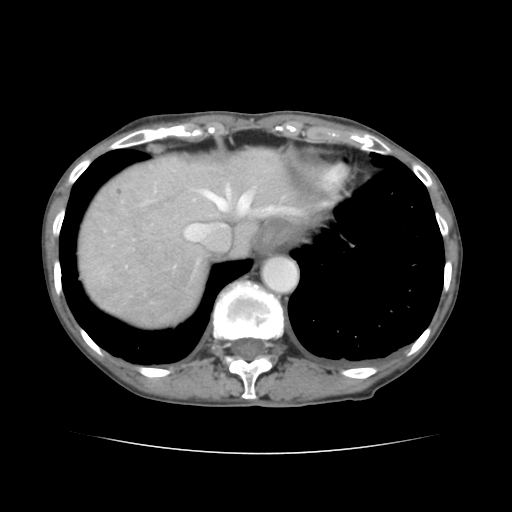
Contrast-enhanced abdominal CT, one axial slice. Position 121 of 136 along the scan axis. 120 kVp. Intravenous contrast given. Soft-tissue window (W 400 / L 40 HU). 2.5 mm slice thickness. 512 × 512 image matrix, field of view 319 × 319 mm. Female patient, age 77 years. From the clinical record (not read from this slice): diagnosis: colorectal cancer liver metastases, imaged before liver resection; multiple liver metastases: yes; largest metastasis: 3 cm; disease in both lobes: no.
Outlined on this slice (expert manual segmentation):
- hepatic veins: box from (x=183, y=183) to (x=280, y=243) px
- liver: (x=79, y=149)–(x=302, y=326)
- planned liver remnant (the part of the liver to remain after resection): (x=179, y=150)–(x=306, y=253)